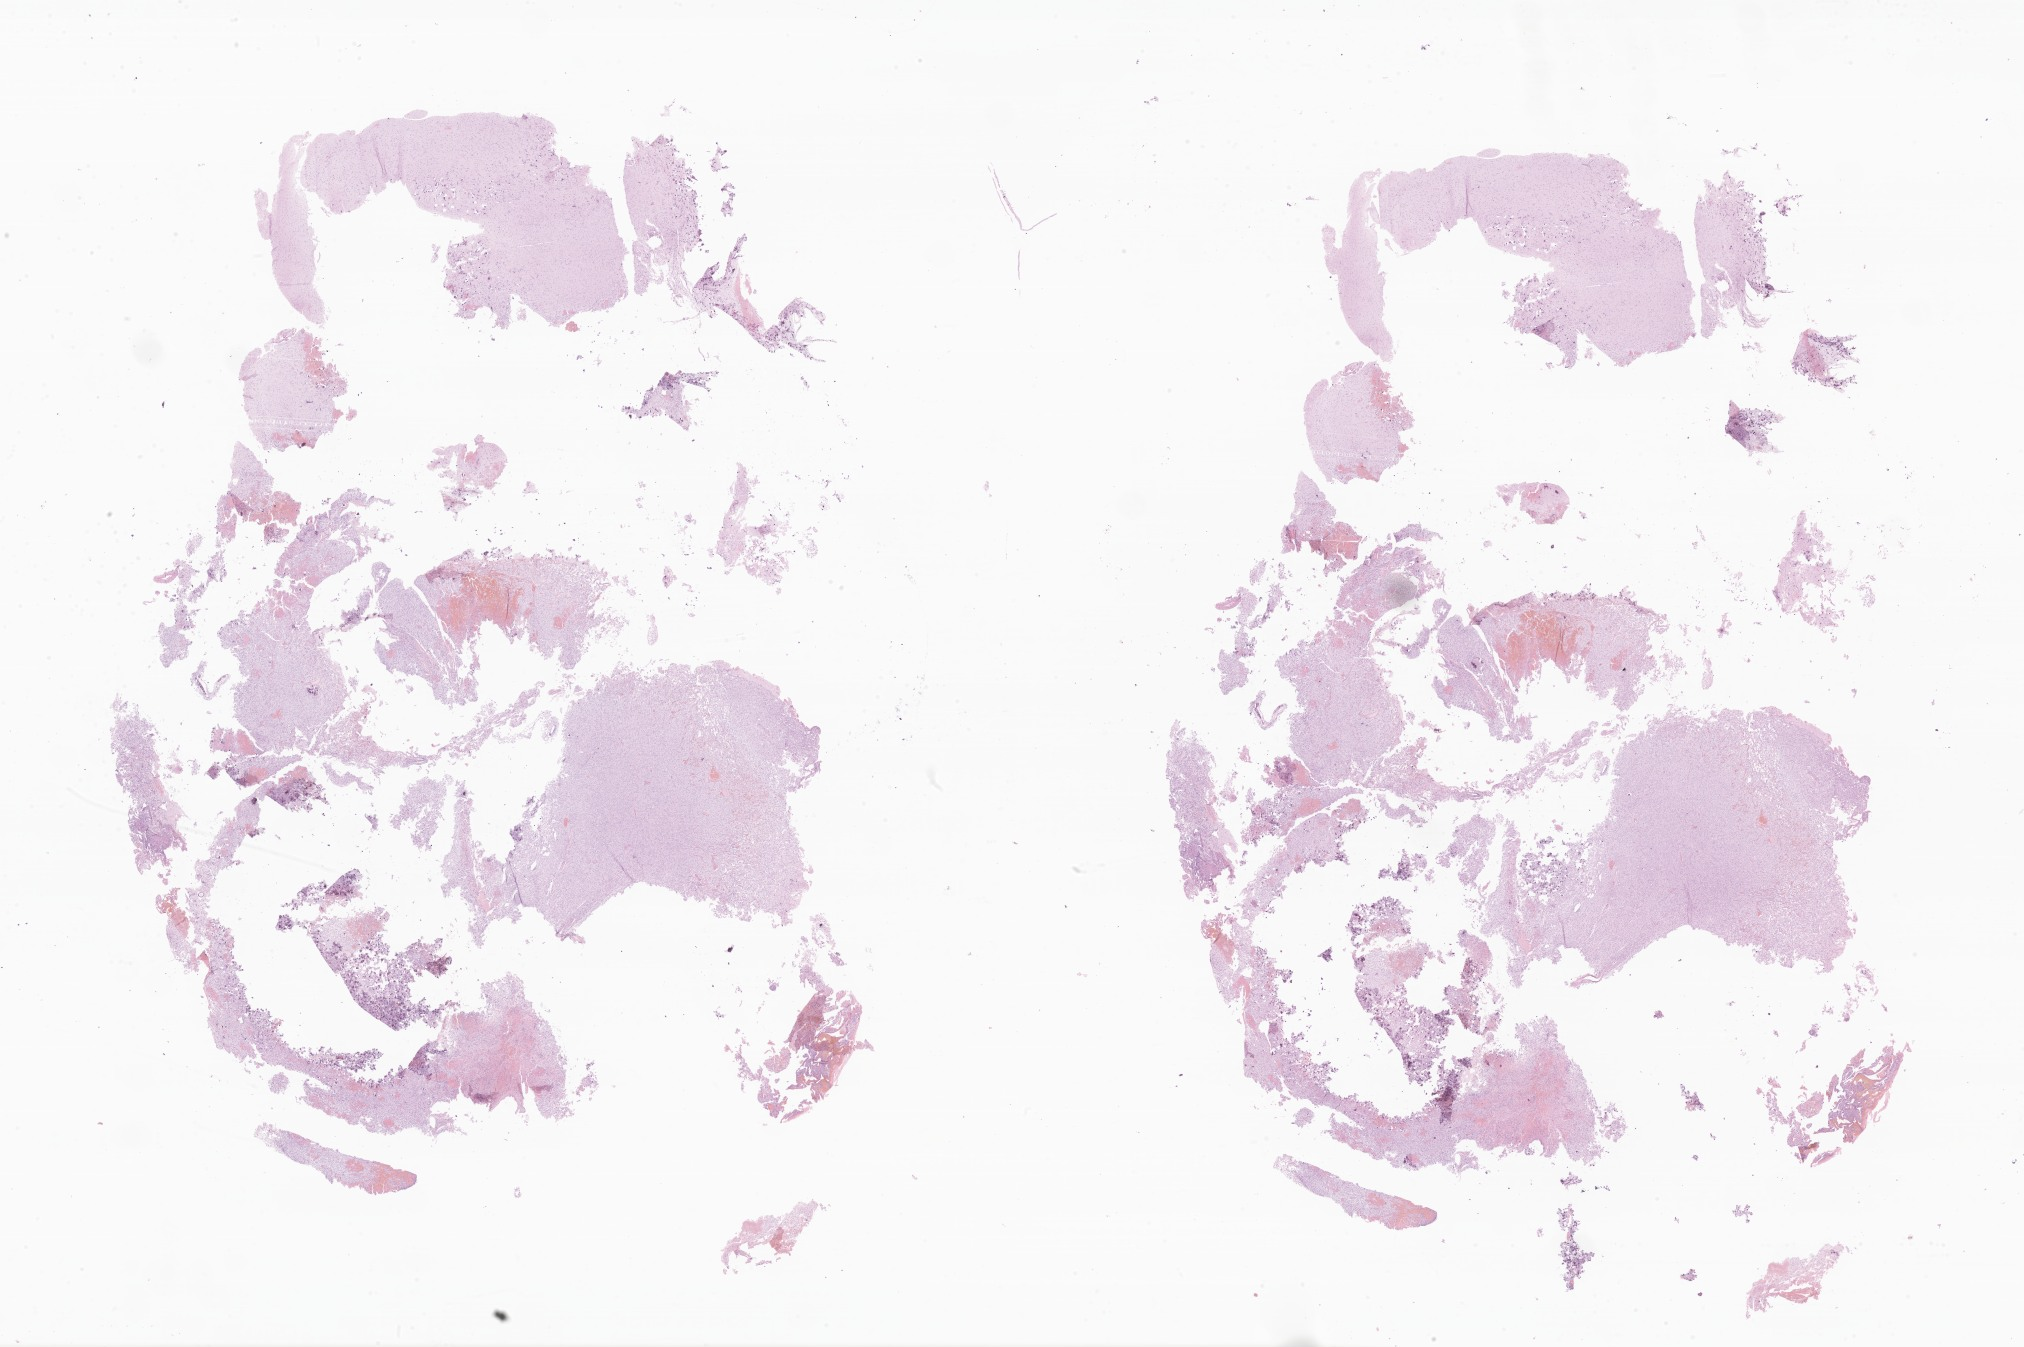
Haematoxylin and eosin whole-slide image of tumor tissue from the brain, a low-resolution overview of the entire scanned area, about 34.1 x 22.7 mm, formalin-fixed, paraffin-embedded (FFPE) tissue. Patient: male, age 204 months (17 years).
Diagnosis (ICD-O-3 morphology term): Glioma, malignant.